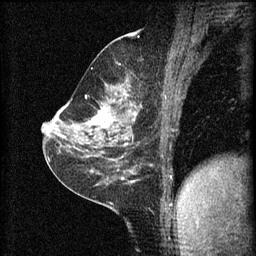
Breast MRI (dynamic contrast-enhanced), one sagittal slice. Position 35 of 60 along the scan axis. 3 images stored at this slice position (order not interpretable as contrast timing). 1.5 T. TE 4.2 ms, TR 8.2 ms. 2 mm slice thickness. 256 × 256 image matrix. Female patient, age 59 years.
Structures marked on this image (semi-automatically segmented with operator editing):
- analysis volume of interest (the breast-tissue region the enhancement analysis was run in; not a lesion): bounding box [x1, y1, x2, y2] px = [78, 92, 137, 135]
- tumour enhancement mask (voxels above the 70 % enhancement threshold inside the analysis volume of interest): [92, 108, 111, 129]